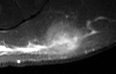
MRI of an extremity soft-tissue mass, one axial slice; slice 25 of 36 in the series (ordered by position); STIR; MR volume resampled by the dataset authors to the PET/CT grid (not the native acquisition matrix); 116 × 74 image matrix, field of view 113 × 72 mm. Male patient. Case-level facts recorded for this patient, not image findings: histological type: pleiomorphic leiomyosarcoma; grade: high; site of the primary tumour: left buttock.
Annotated regions visible in this slice (expert contour drawn on MRI and transferred to this co-registered scan by the dataset authors):
- gross tumour volume including surrounding oedema: bounding box <44,24,76,54> (left, top, right, bottom; pixels)
- gross tumour volume (mass): <44,28,72,52>